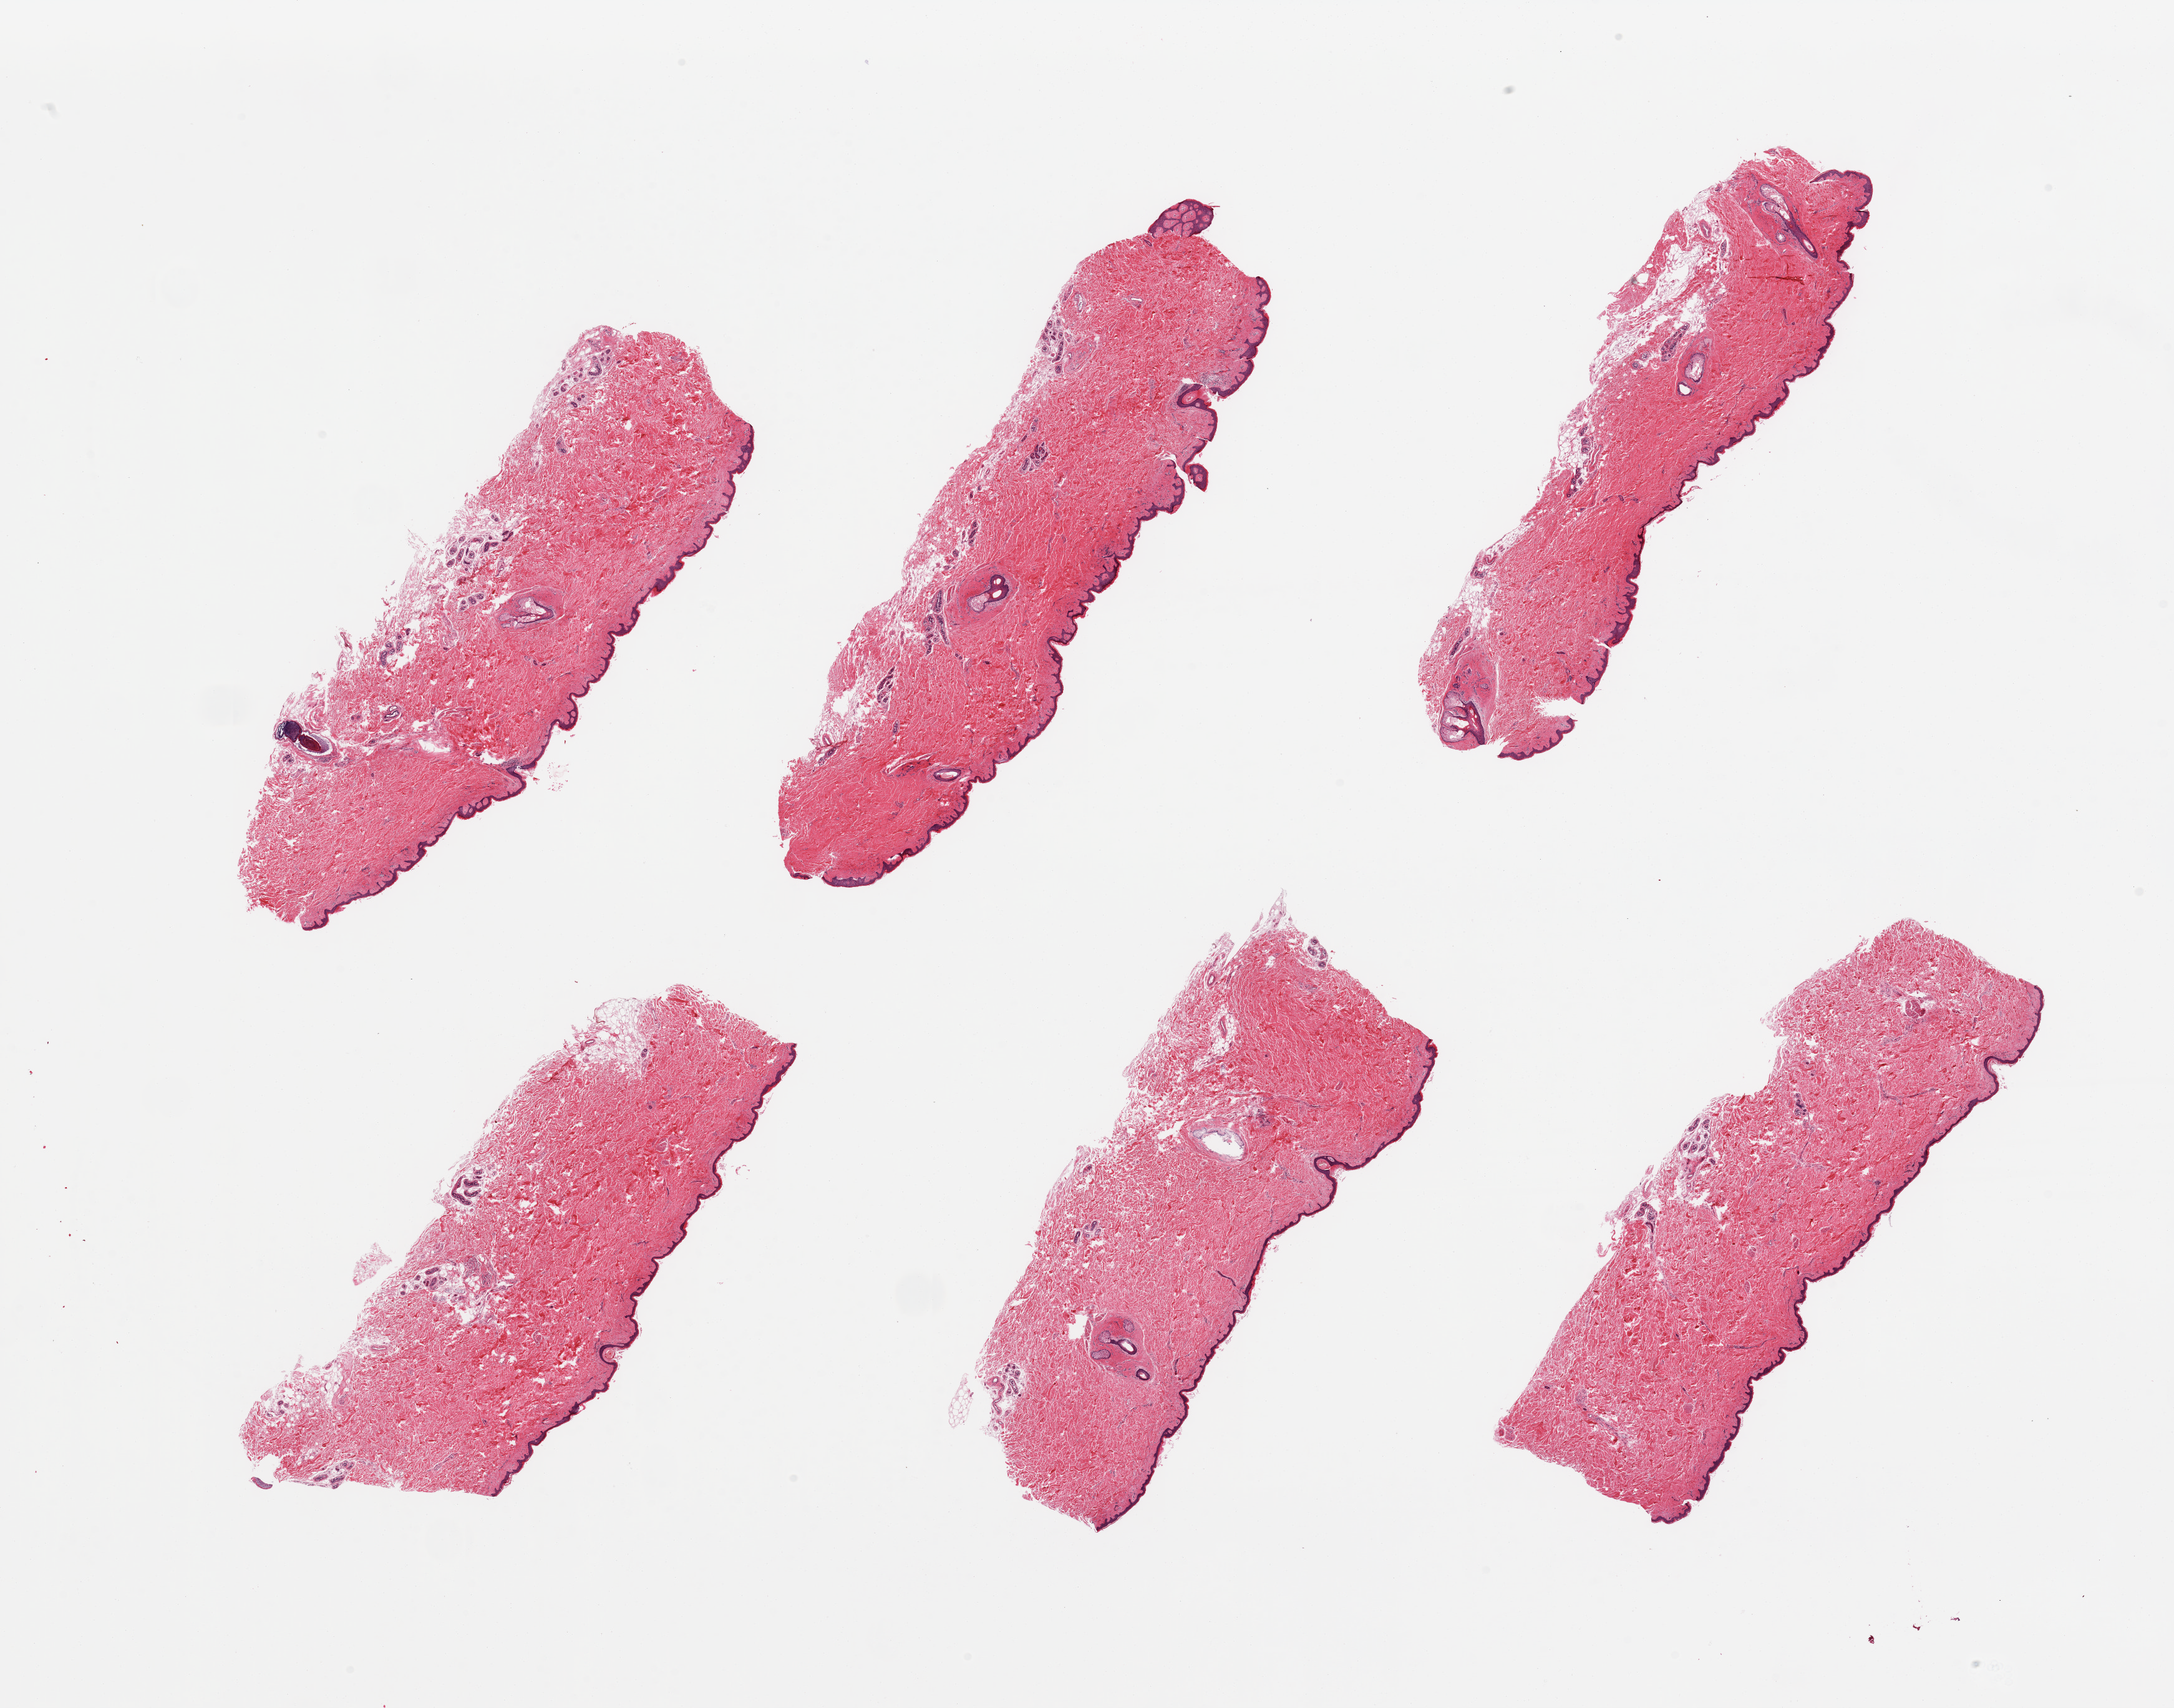
Digitized haematoxylin and eosin-stained section, shown as a low-resolution overview of the whole scanned area (about 27.6 x 21.7 mm); PAXgene-fixed, paraffin-embedded tissue; section of skin of suprapubic region (target tissue); tissue donor sample. Donor: male.
Review note (as recorded): 6 pieces; 10% internal fat.